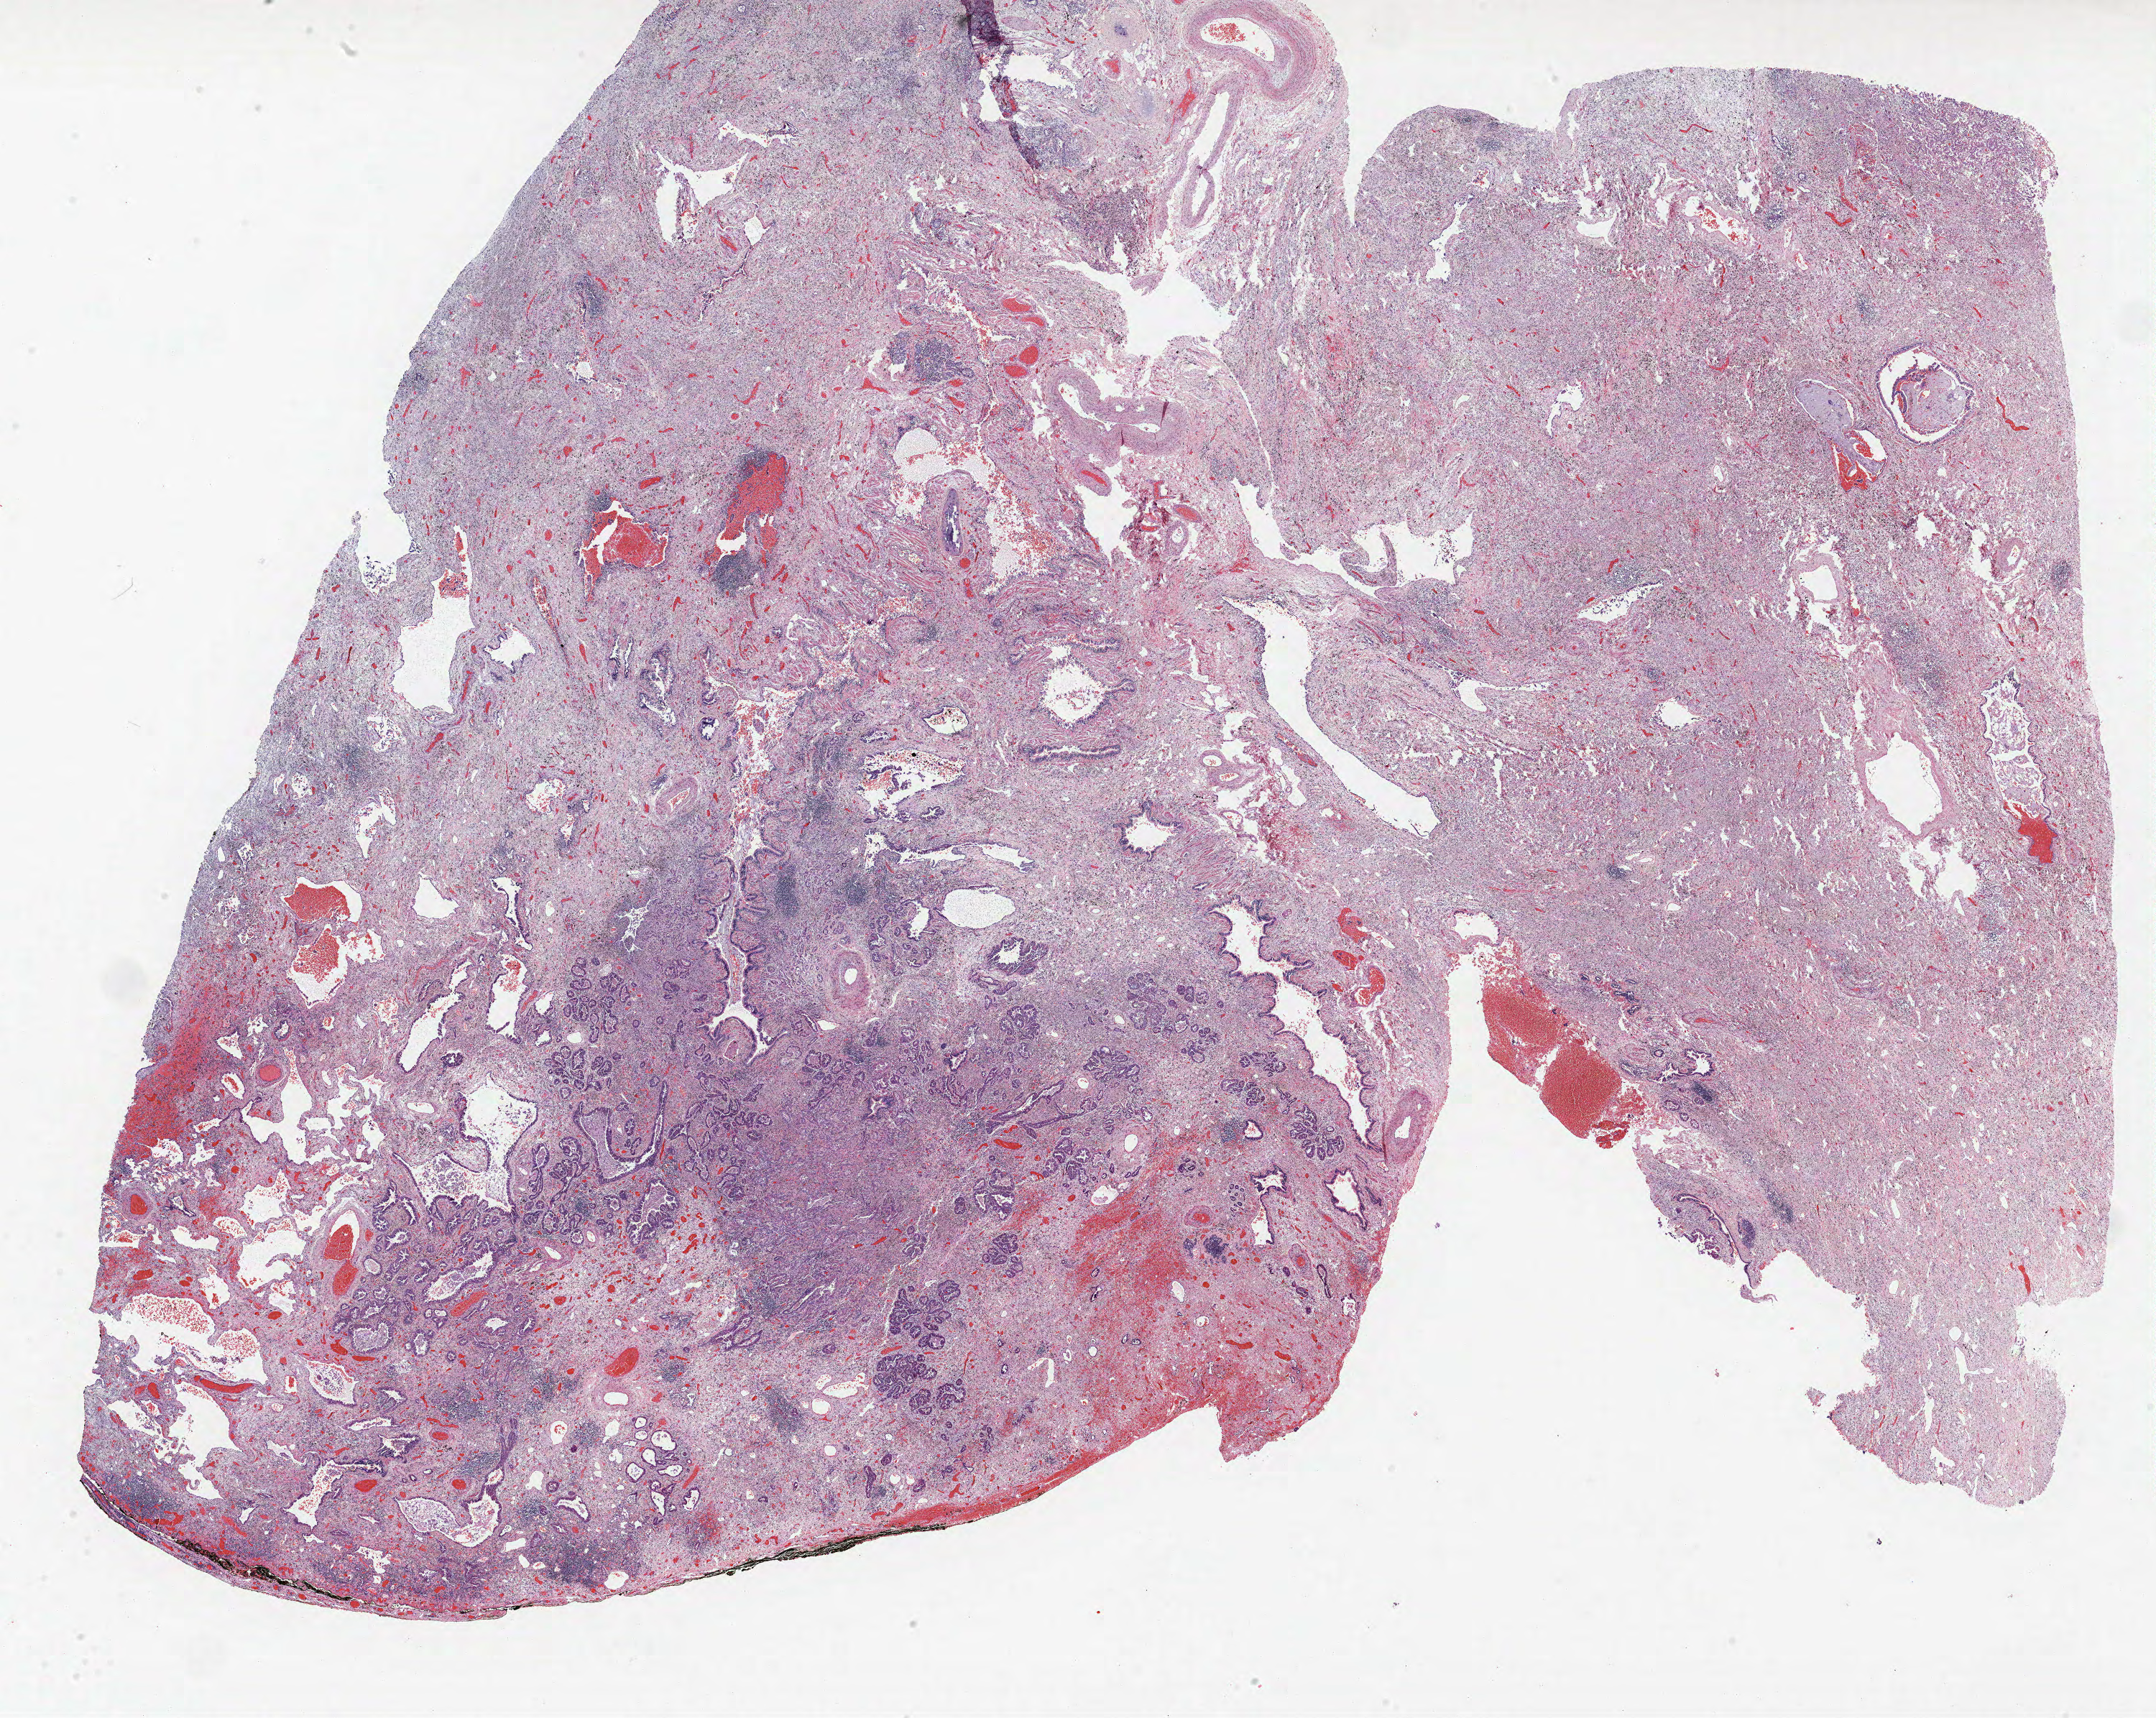
Whole-slide histology image, H&E, low-resolution overview of the scanned area, about 24.0 x 19.1 mm; FFPE section; lung. Female patient, aged 61 at enrolment. Current smoker at enrolment. Grade: well differentiated (G1).
- participant's lung-cancer diagnosis: Adenocarcinoma, NOS
- ICD-O-3 topography: upper lobe of lung (C34.1)
- primary tumour location (clinical record): right upper lobe
- stage (AJCC 6th edition): IIIB
- tumour size (pathology): 30 mm
- note: participant had 2 primary lung cancers recorded; fields above describe the first